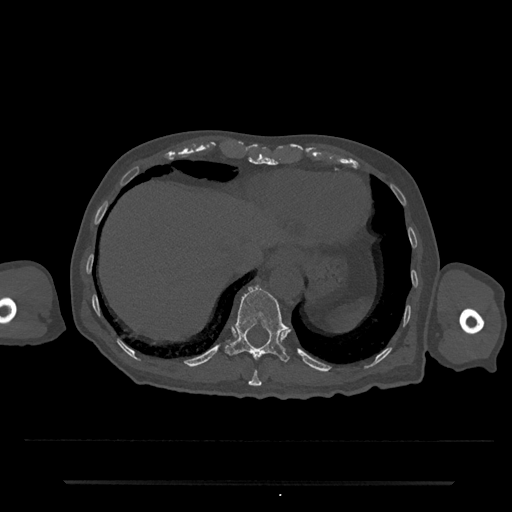
CT including the spine, one axial slice; position 262 of 797 along the scan axis; bone window (W 1800 / L 400 HU); 0.5 mm slice thickness; 512 × 512 image matrix, field of view 427 × 427 mm. Male patient, age 74 years. Case-level facts recorded for this patient, not image findings: primary cancer: prostate.
Outlined on this slice (semi-automatically segmented with operator editing):
- T10 vertebra: bounding box (x1, y1, x2, y2) in pixels: (248, 370, 262, 386)
- T11 vertebra: (225, 285, 290, 362)